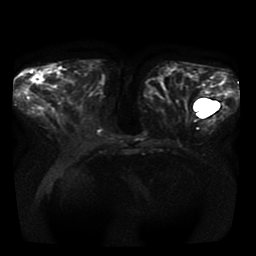
Breast MRI, one axial slice. Slice 14 of 41 in the series (ordered by position). Diffusion-weighted series; image 2 of 4 stored at this slice position (different b-values; order by instance number). 1.5 T. 256 × 256 image matrix, field of view 350 × 350 mm. Female patient.
Outlined on this slice (expert manual segmentation):
- tumour on diffusion-weighted imaging: box from (x=28, y=71) to (x=41, y=85) px